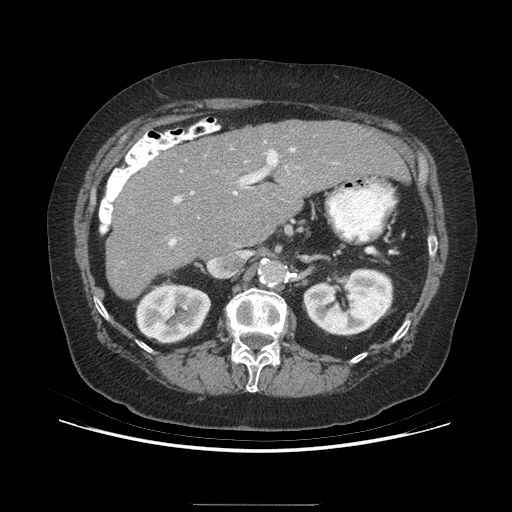
Contrast-enhanced abdominal CT (liver protocol), one axial slice. Position 152 of 192 along the scan axis. Reconstruction kernel STANDARD. 140 kVp. Soft-tissue window (W 400 / L 40 HU). 2.5 mm slice thickness. 512 × 512 image matrix, field of view 400 × 400 mm. From the clinical record (not read from this slice): diagnosis: hepatocellular carcinoma (patient treated with transarterial chemoembolisation; whether this scan precedes or follows treatment is not stated here); TNM stage (as recorded): Stage-I; Child-Pugh class: A; tumour differentiation: moderately differentiated; tumour nodularity: uninodular.
Structures marked on this image (semi-automatically segmented with operator editing):
- liver parenchyma outside the tumour (the mass and vessels are separate outlines, so this box may not span the whole liver): bounding box <106,120,406,298> (left, top, right, bottom; pixels)
- liver vessels: <169,148,295,246>